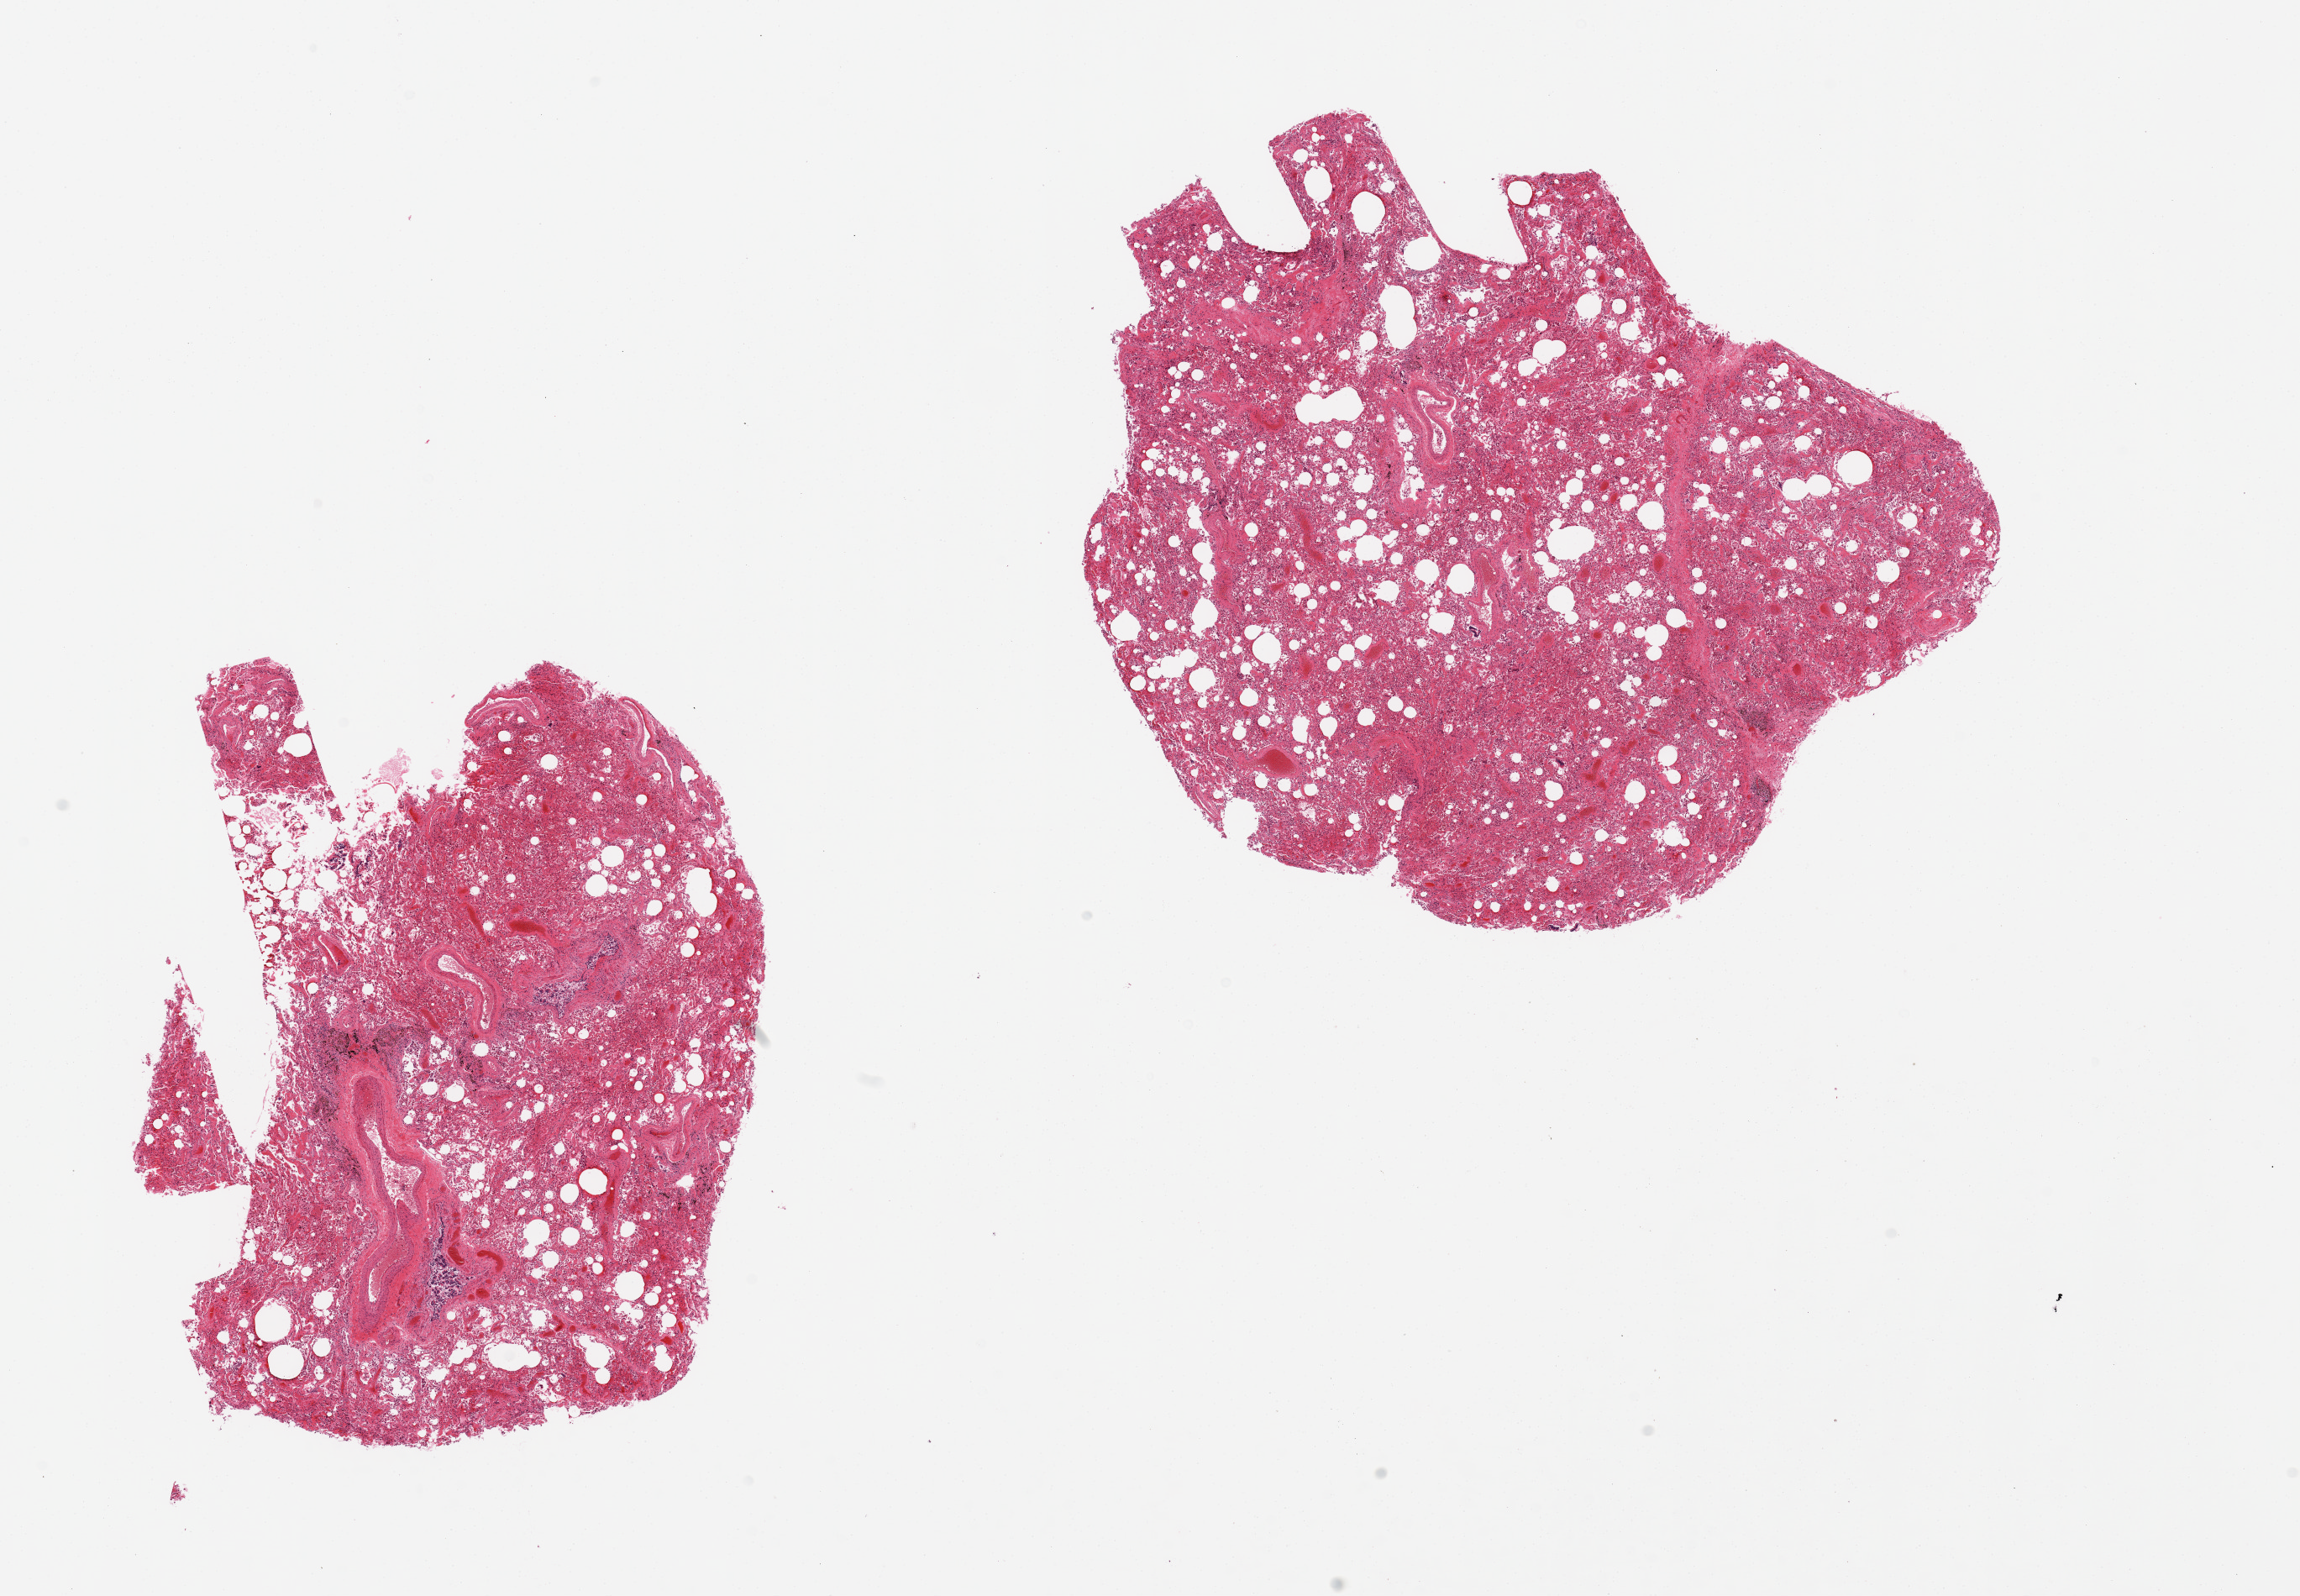
Digitized haematoxylin and eosin-stained section, shown as a low-resolution overview of the whole scanned area (about 21.7 x 15.0 mm, acquisition: 20x scan); PAXgene-fixed, paraffin-embedded tissue; section of lung (target tissue); tissue donor sample. Male donor.
Pathologist's review note for this sample: 2 pieces, some congestion and edema, numerous hemosiderin-laden macrophages, fibrosis.